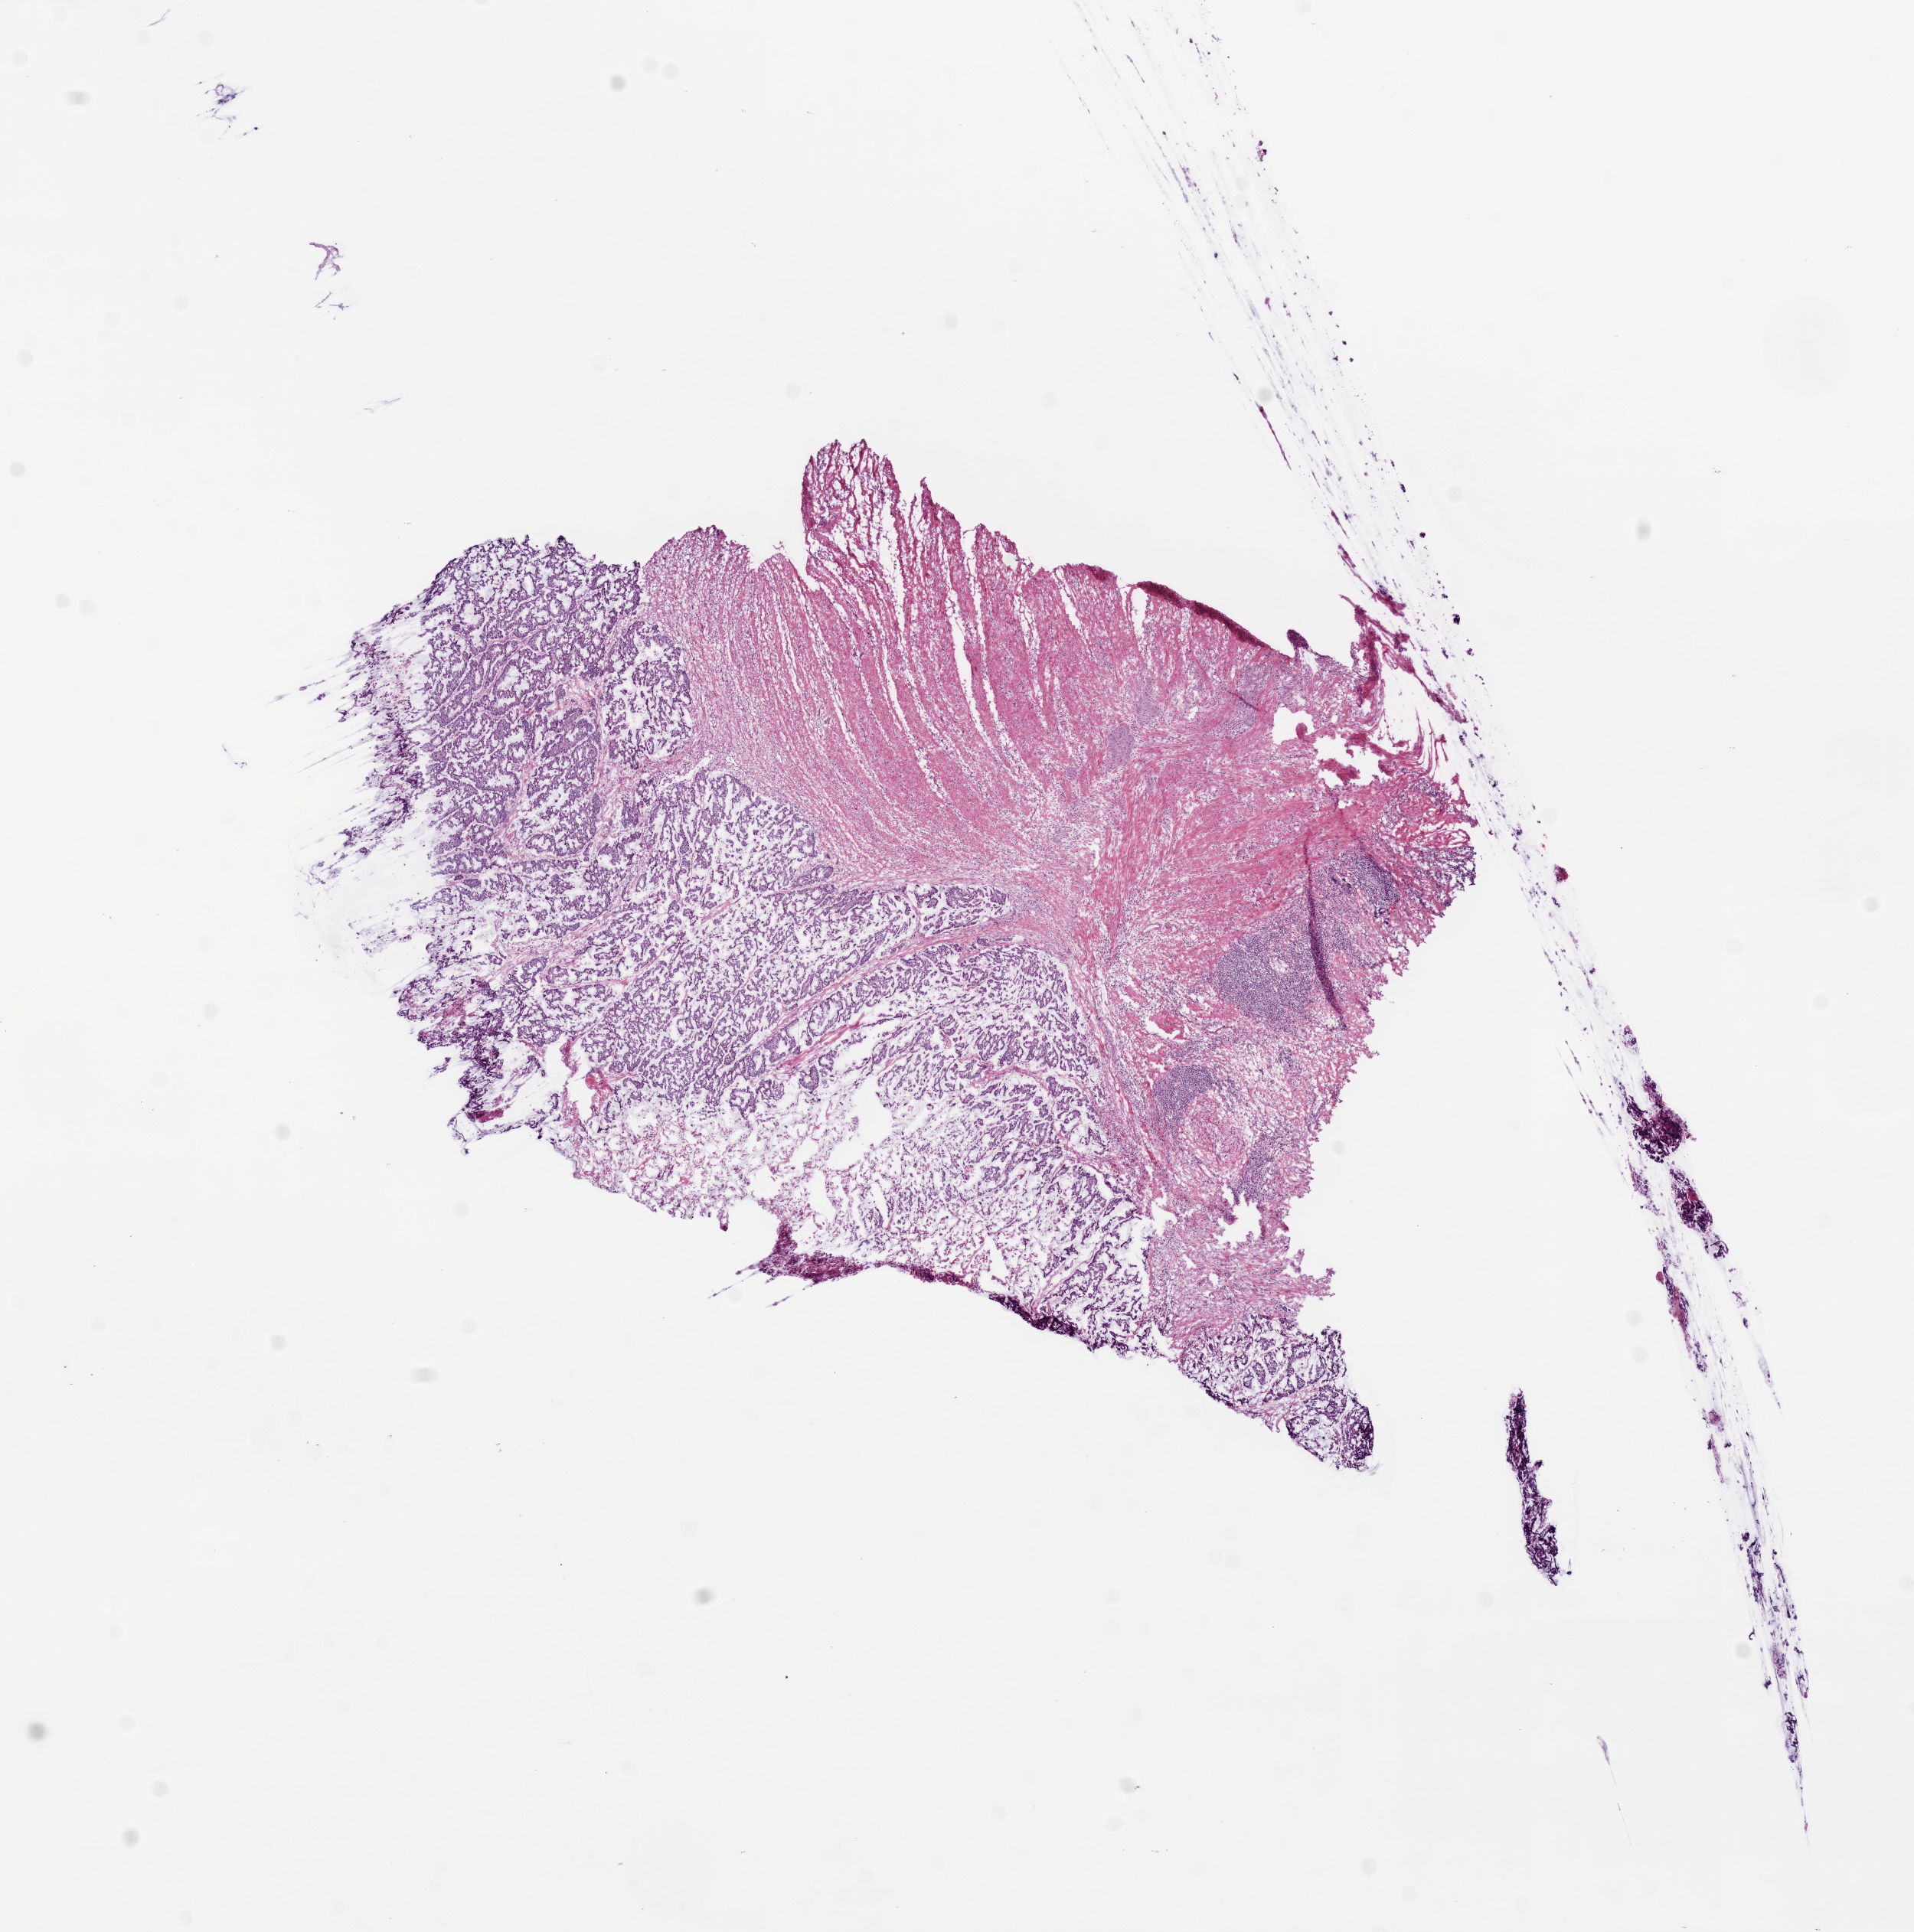
Whole-slide histology image, Hematoxylin and eosin (H&E) stained, low-resolution overview of the scanned area, about 10.0 x 10.1 mm (slide scanned at 20x), frozen section from the top of the tissue portion, rectum, primary tumour sample. Patient: female, age at initial diagnosis 83 years. Pathologist review of this section (percent, as recorded): tumour cells 47%, tumour nuclei 65%, normal cells 53%, stromal cells 2%, necrosis 1%.
* AJCC pathologic stage: IIA (6th edition)
* pathologic diagnosis: Mucinous adenocarcinoma (unknown primary site)
* TNM: T3 N0 M0